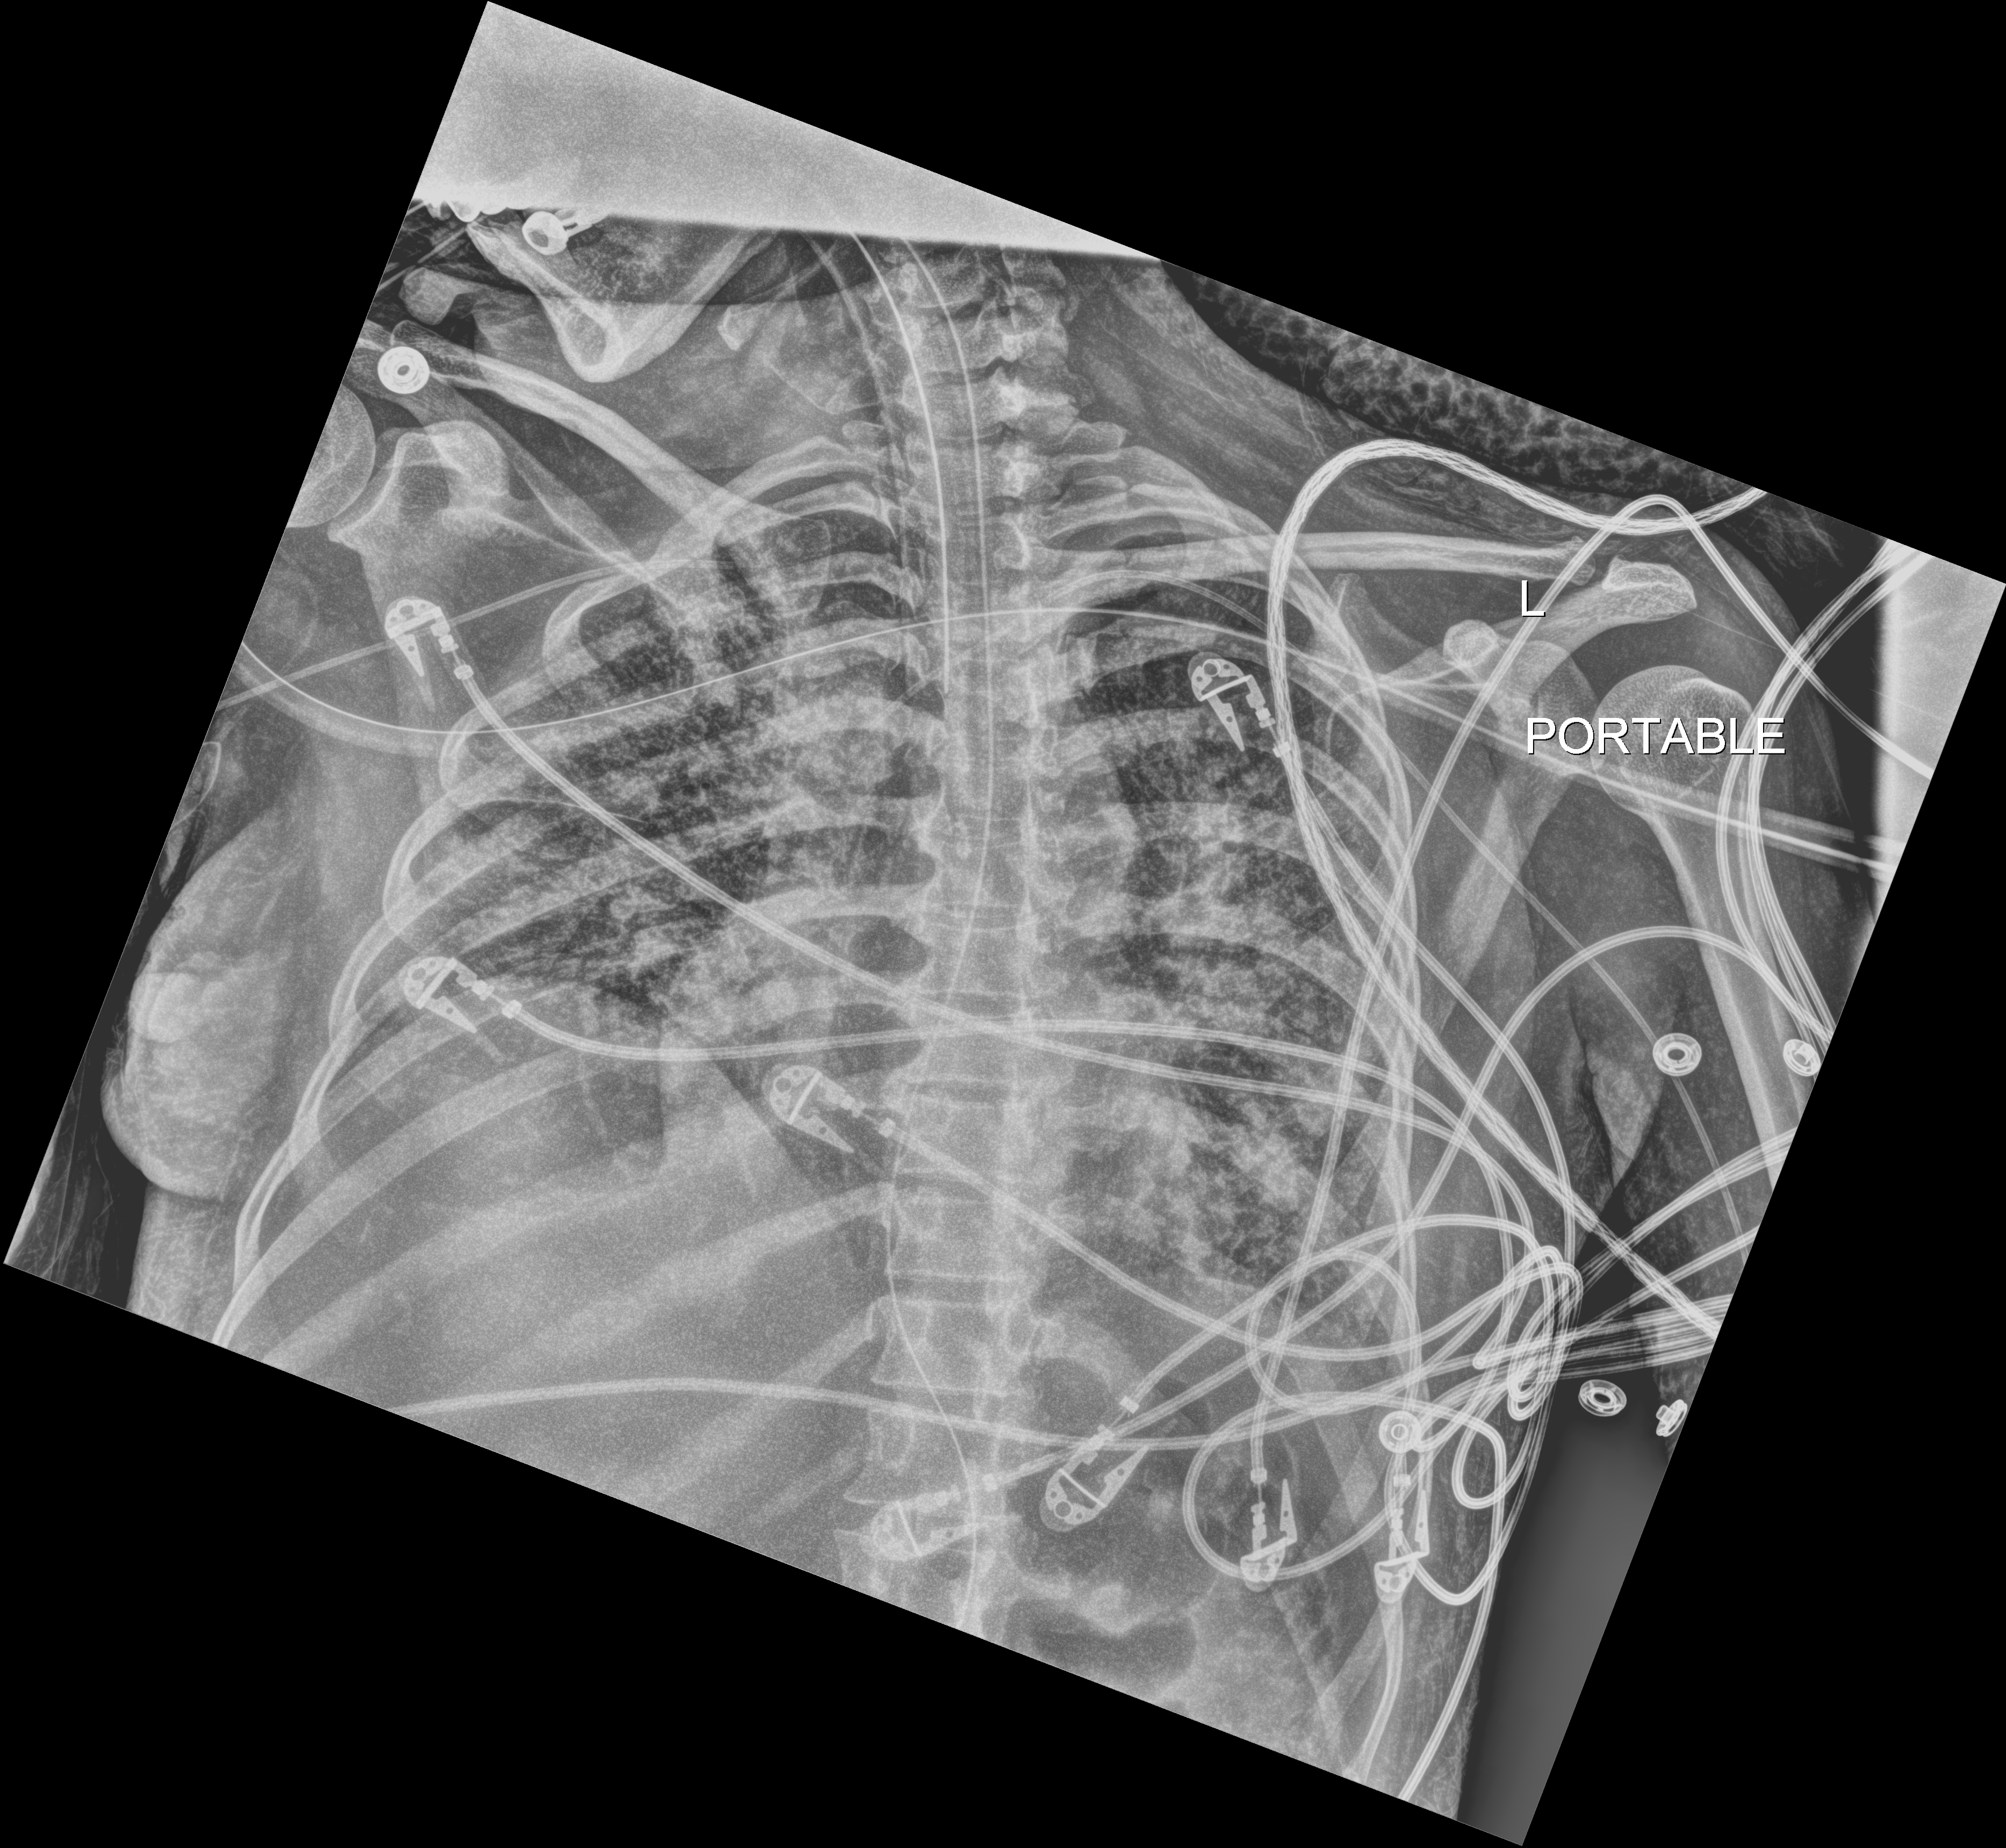
Bedside chest radiograph (digital radiography); anteroposterior (AP) projection. Female patient hospitalised with COVID-19, age 18–59 years.
Admission-level facts for this patient (not findings on this image; timing relative to this image not recorded): length of hospital stay: 71 days.